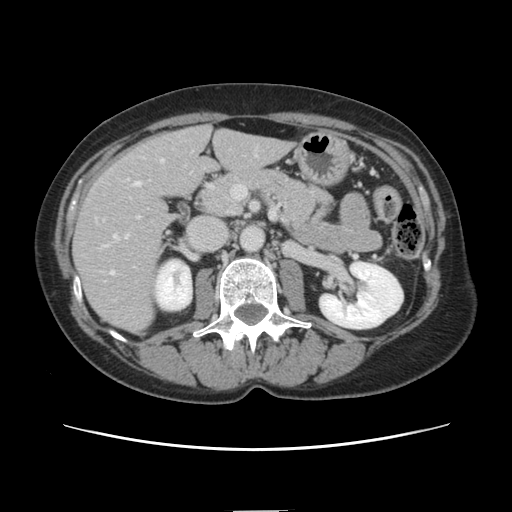
Contrast-enhanced abdominal CT, one axial slice. Slice 58 of 141 in the series (ordered by position). Intravenous contrast given. Soft-tissue window (W 400 / L 40 HU). 512 × 512 image matrix, field of view 350 × 350 mm. Female patient, age 63 years. From the clinical record (not read from this slice): diagnosis: colorectal cancer liver metastases, imaged before liver resection; multiple liver metastases: yes; largest metastasis: 3.2 cm; chemotherapy before resection: yes.
Structures marked on this image (expert manual segmentation):
- hepatic veins: bounding box [x1, y1, x2, y2] px = [109, 181, 140, 276]
- liver: [75, 126, 290, 332]
- planned liver remnant (the part of the liver to remain after resection): [177, 127, 290, 186]
- portal vein (with intrahepatic branches): [126, 179, 130, 237]